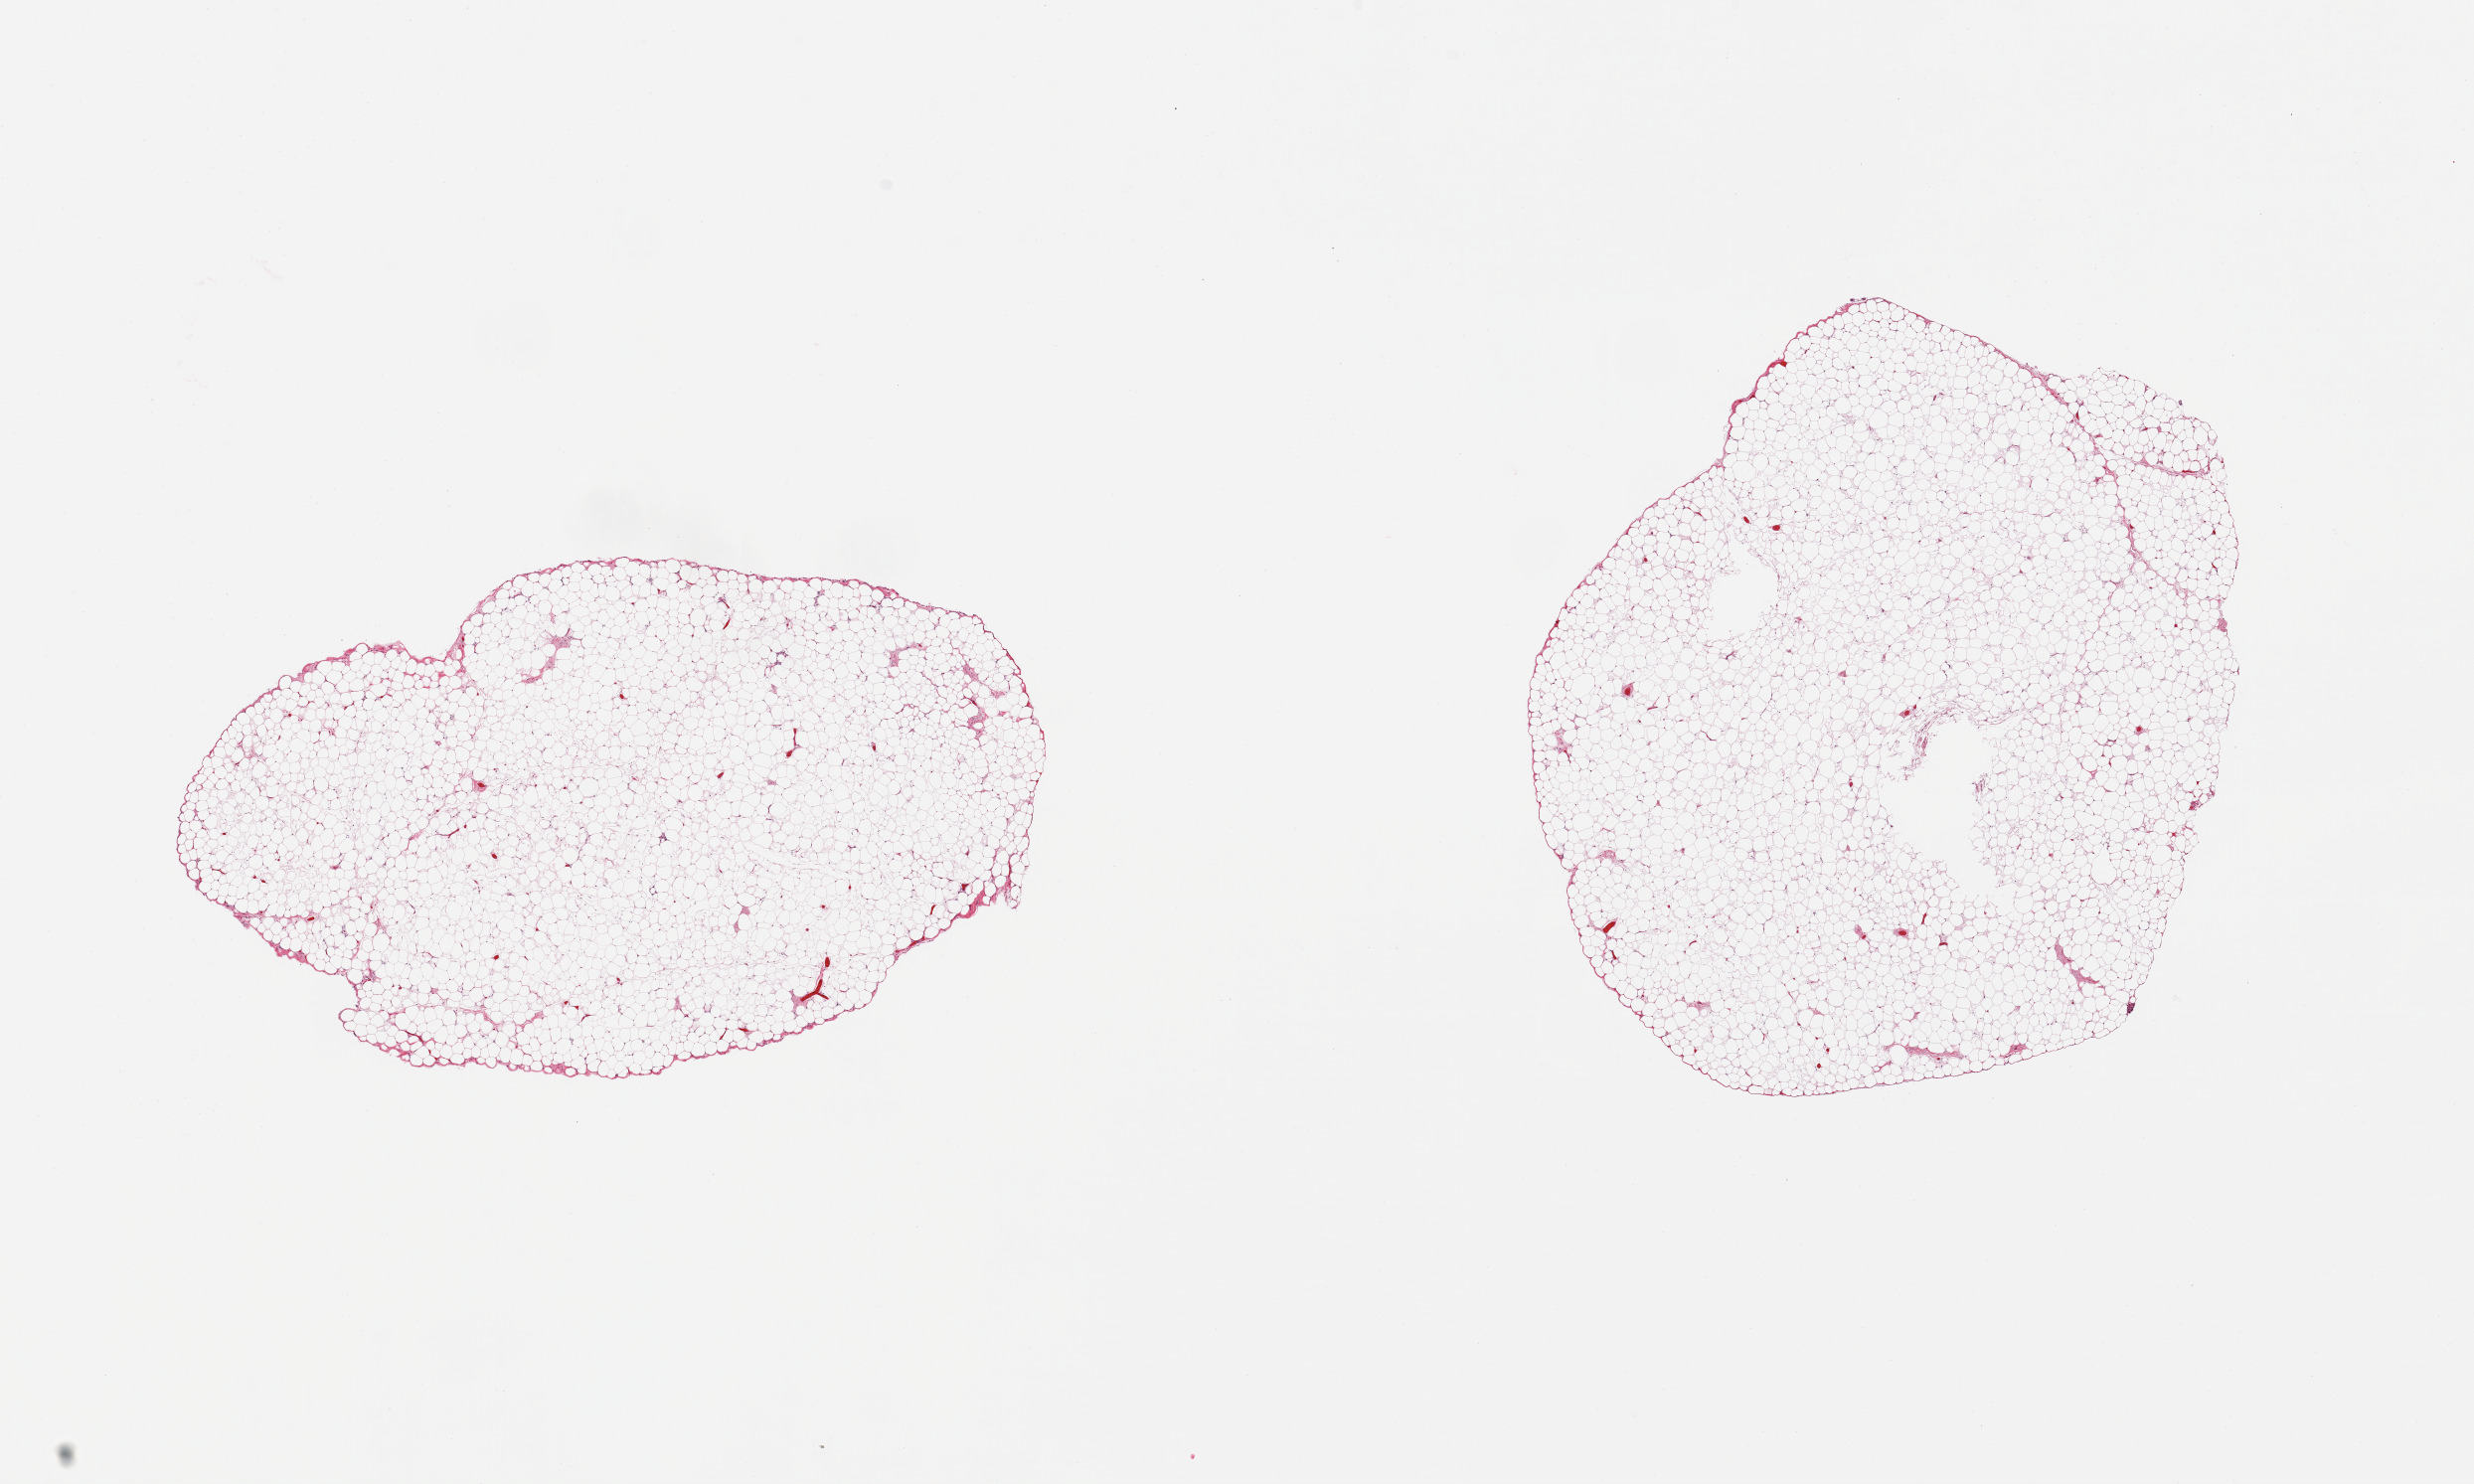
Digitized H&E-stained section — low-resolution overview of the scanned area, about 19.7 x 11.8 mm (slide scanned at 20x). PAXgene-fixed, paraffin-embedded tissue. Target tissue: omentum. Donor tissue sample. Donor sex: male.
Reviewer comment on this tissue sample: 2 pieces, only trace fascia elements.